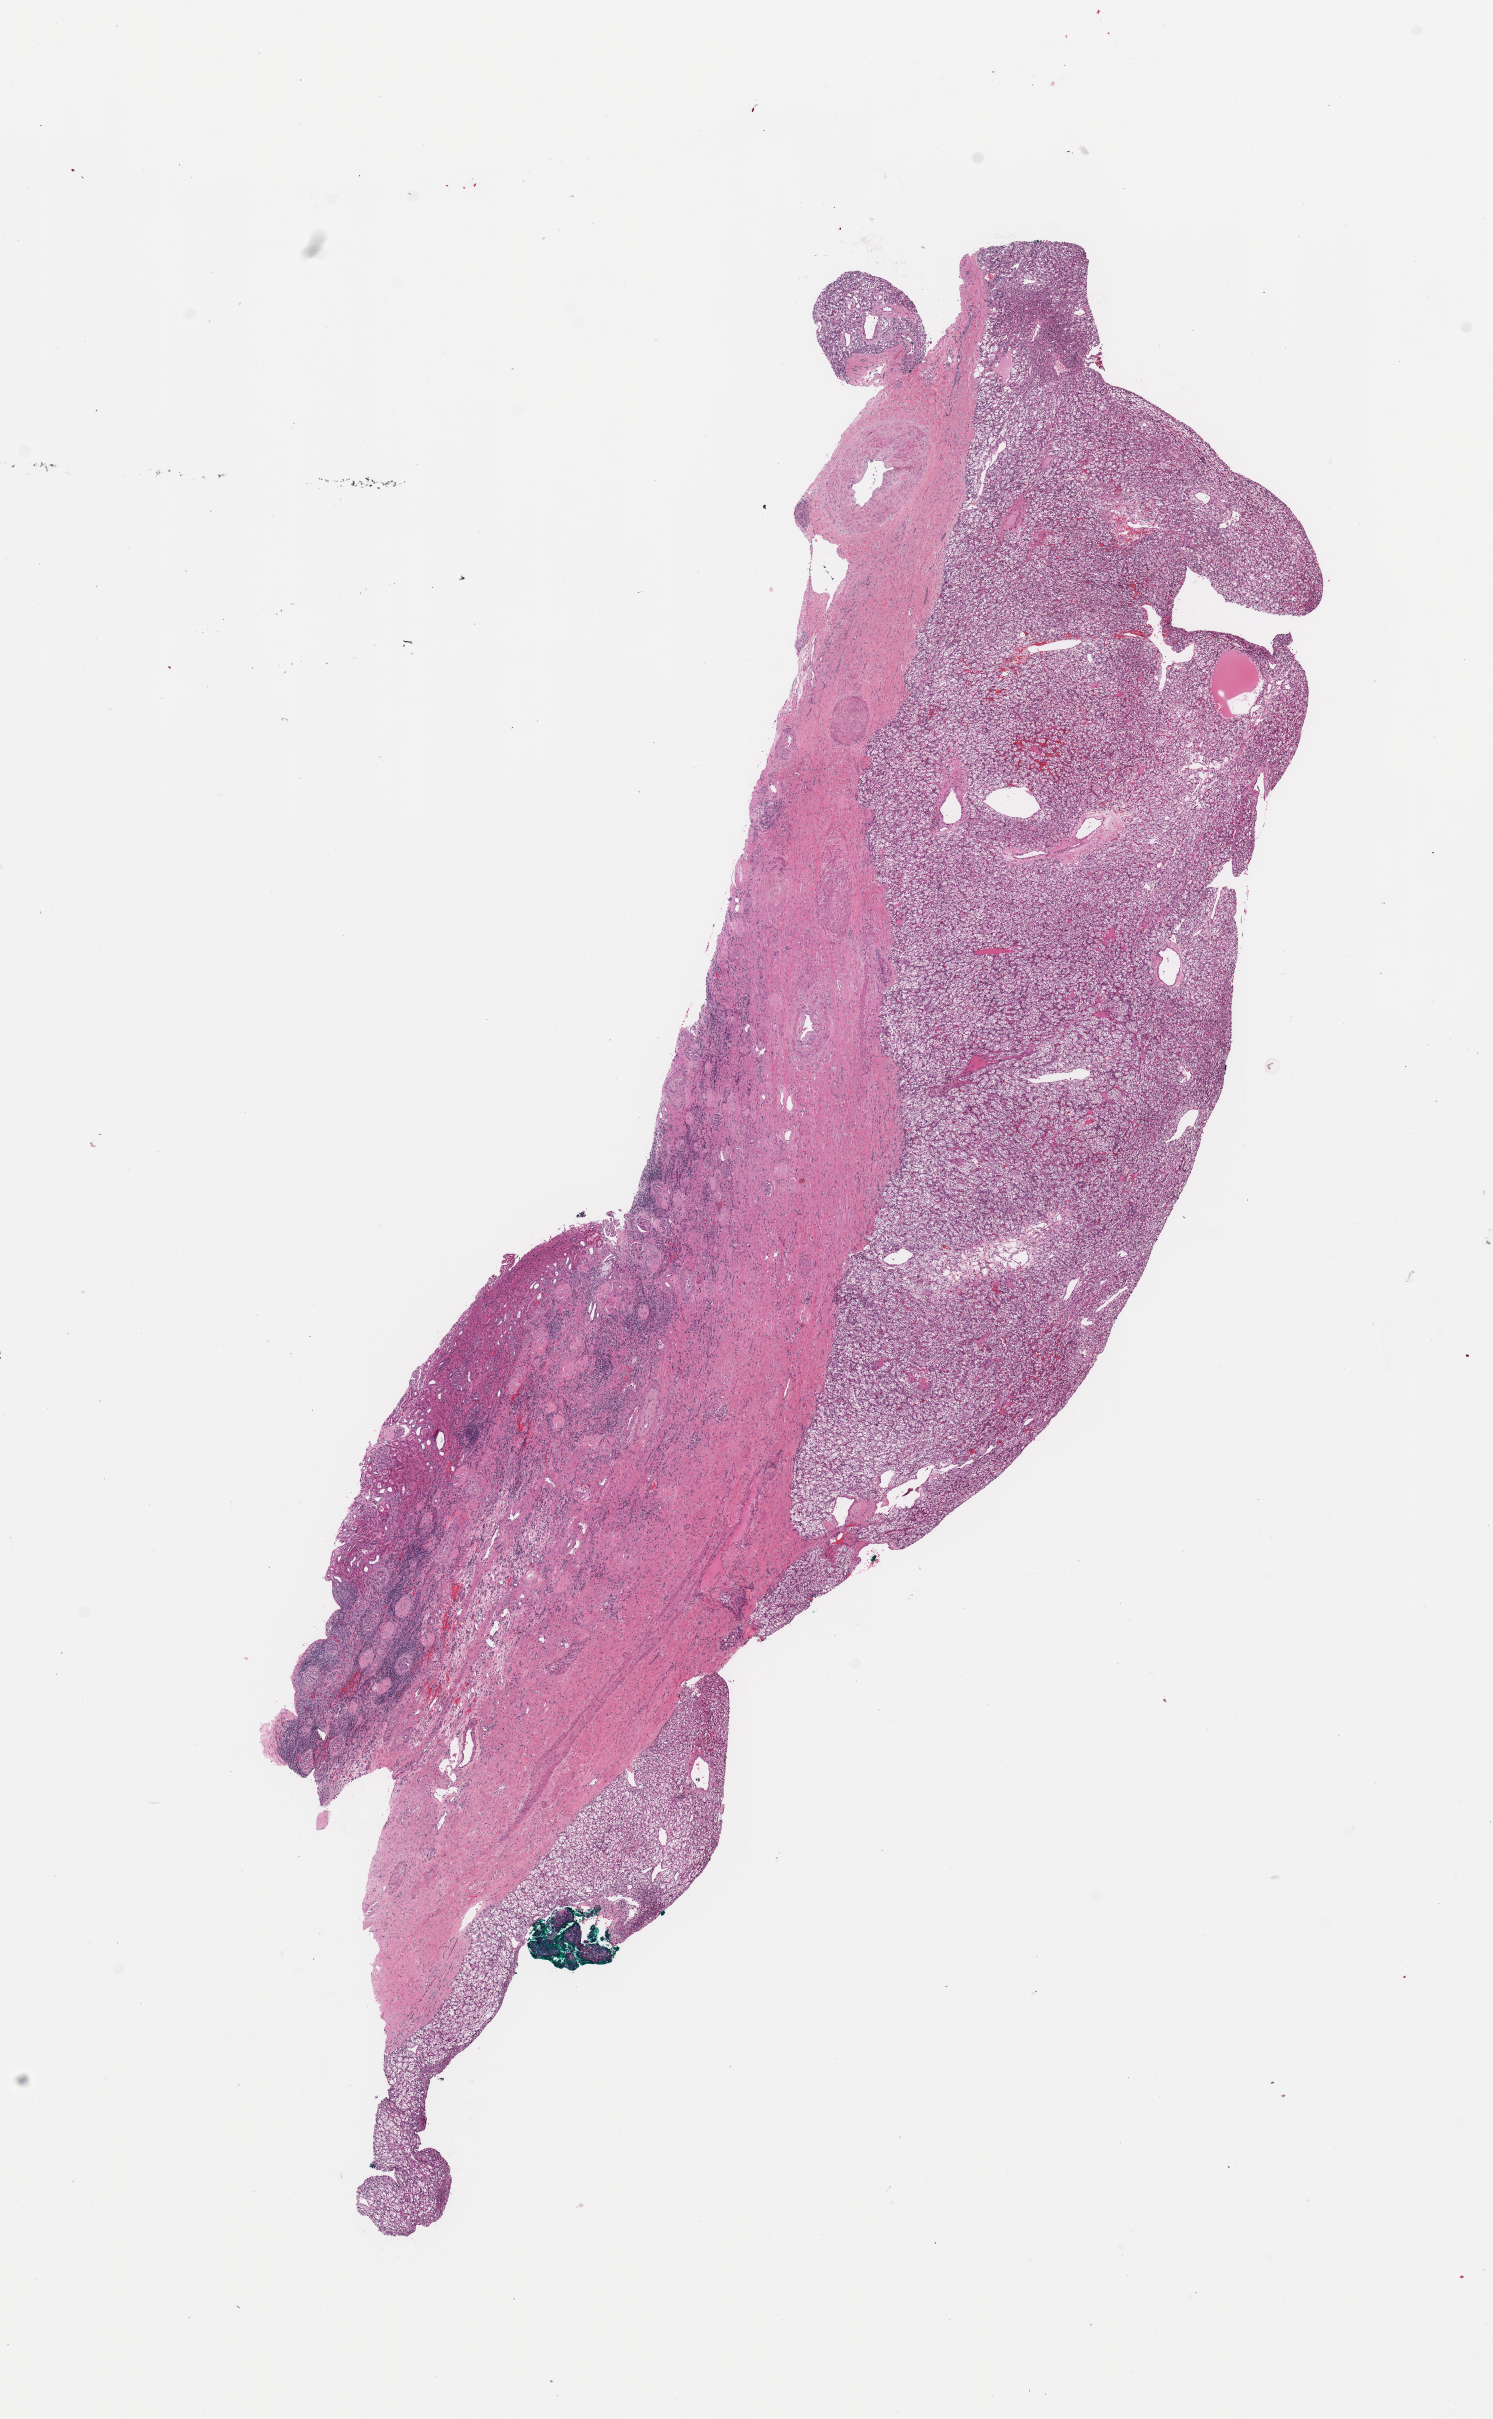
Whole-slide histology image, H&E — low-resolution overview of the scanned area, about 11.8 x 19.1 mm (slide scanned at 20x). Kidney, tumour tissue. Patient: female, age 59 years.
Histologic diagnosis: Renal cell carcinoma, NOS.